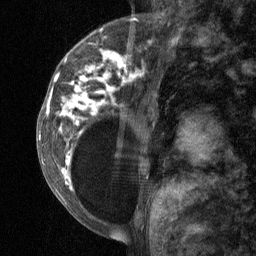
Breast MRI (dynamic contrast-enhanced), one sagittal slice; slice 21 of 64 in the series (ordered by position); dynamic contrast-enhanced study with each time point stored as its own series, time point 2 of 3 at this slice position (early post-contrast, ordered by acquisition time); 1.5 T; TE 4.8 ms, TR 27 ms; 2 mm slice thickness; 256 × 256 image matrix. Patient: female, 34 years. Case-level facts recorded for this patient, not image findings: setting: breast cancer imaged before/during neoadjuvant chemotherapy; receptor status: HR-positive, HER2-negative.
Outlined on this slice (semi-automatically segmented with operator editing):
- analysis volume of interest (the breast-tissue region the enhancement analysis was run in; not a lesion): bounding box <41,23,157,197> (left, top, right, bottom; pixels)
- tumour enhancement mask (voxels above the 90 % enhancement threshold inside the analysis volume of interest): <45,49,144,189>